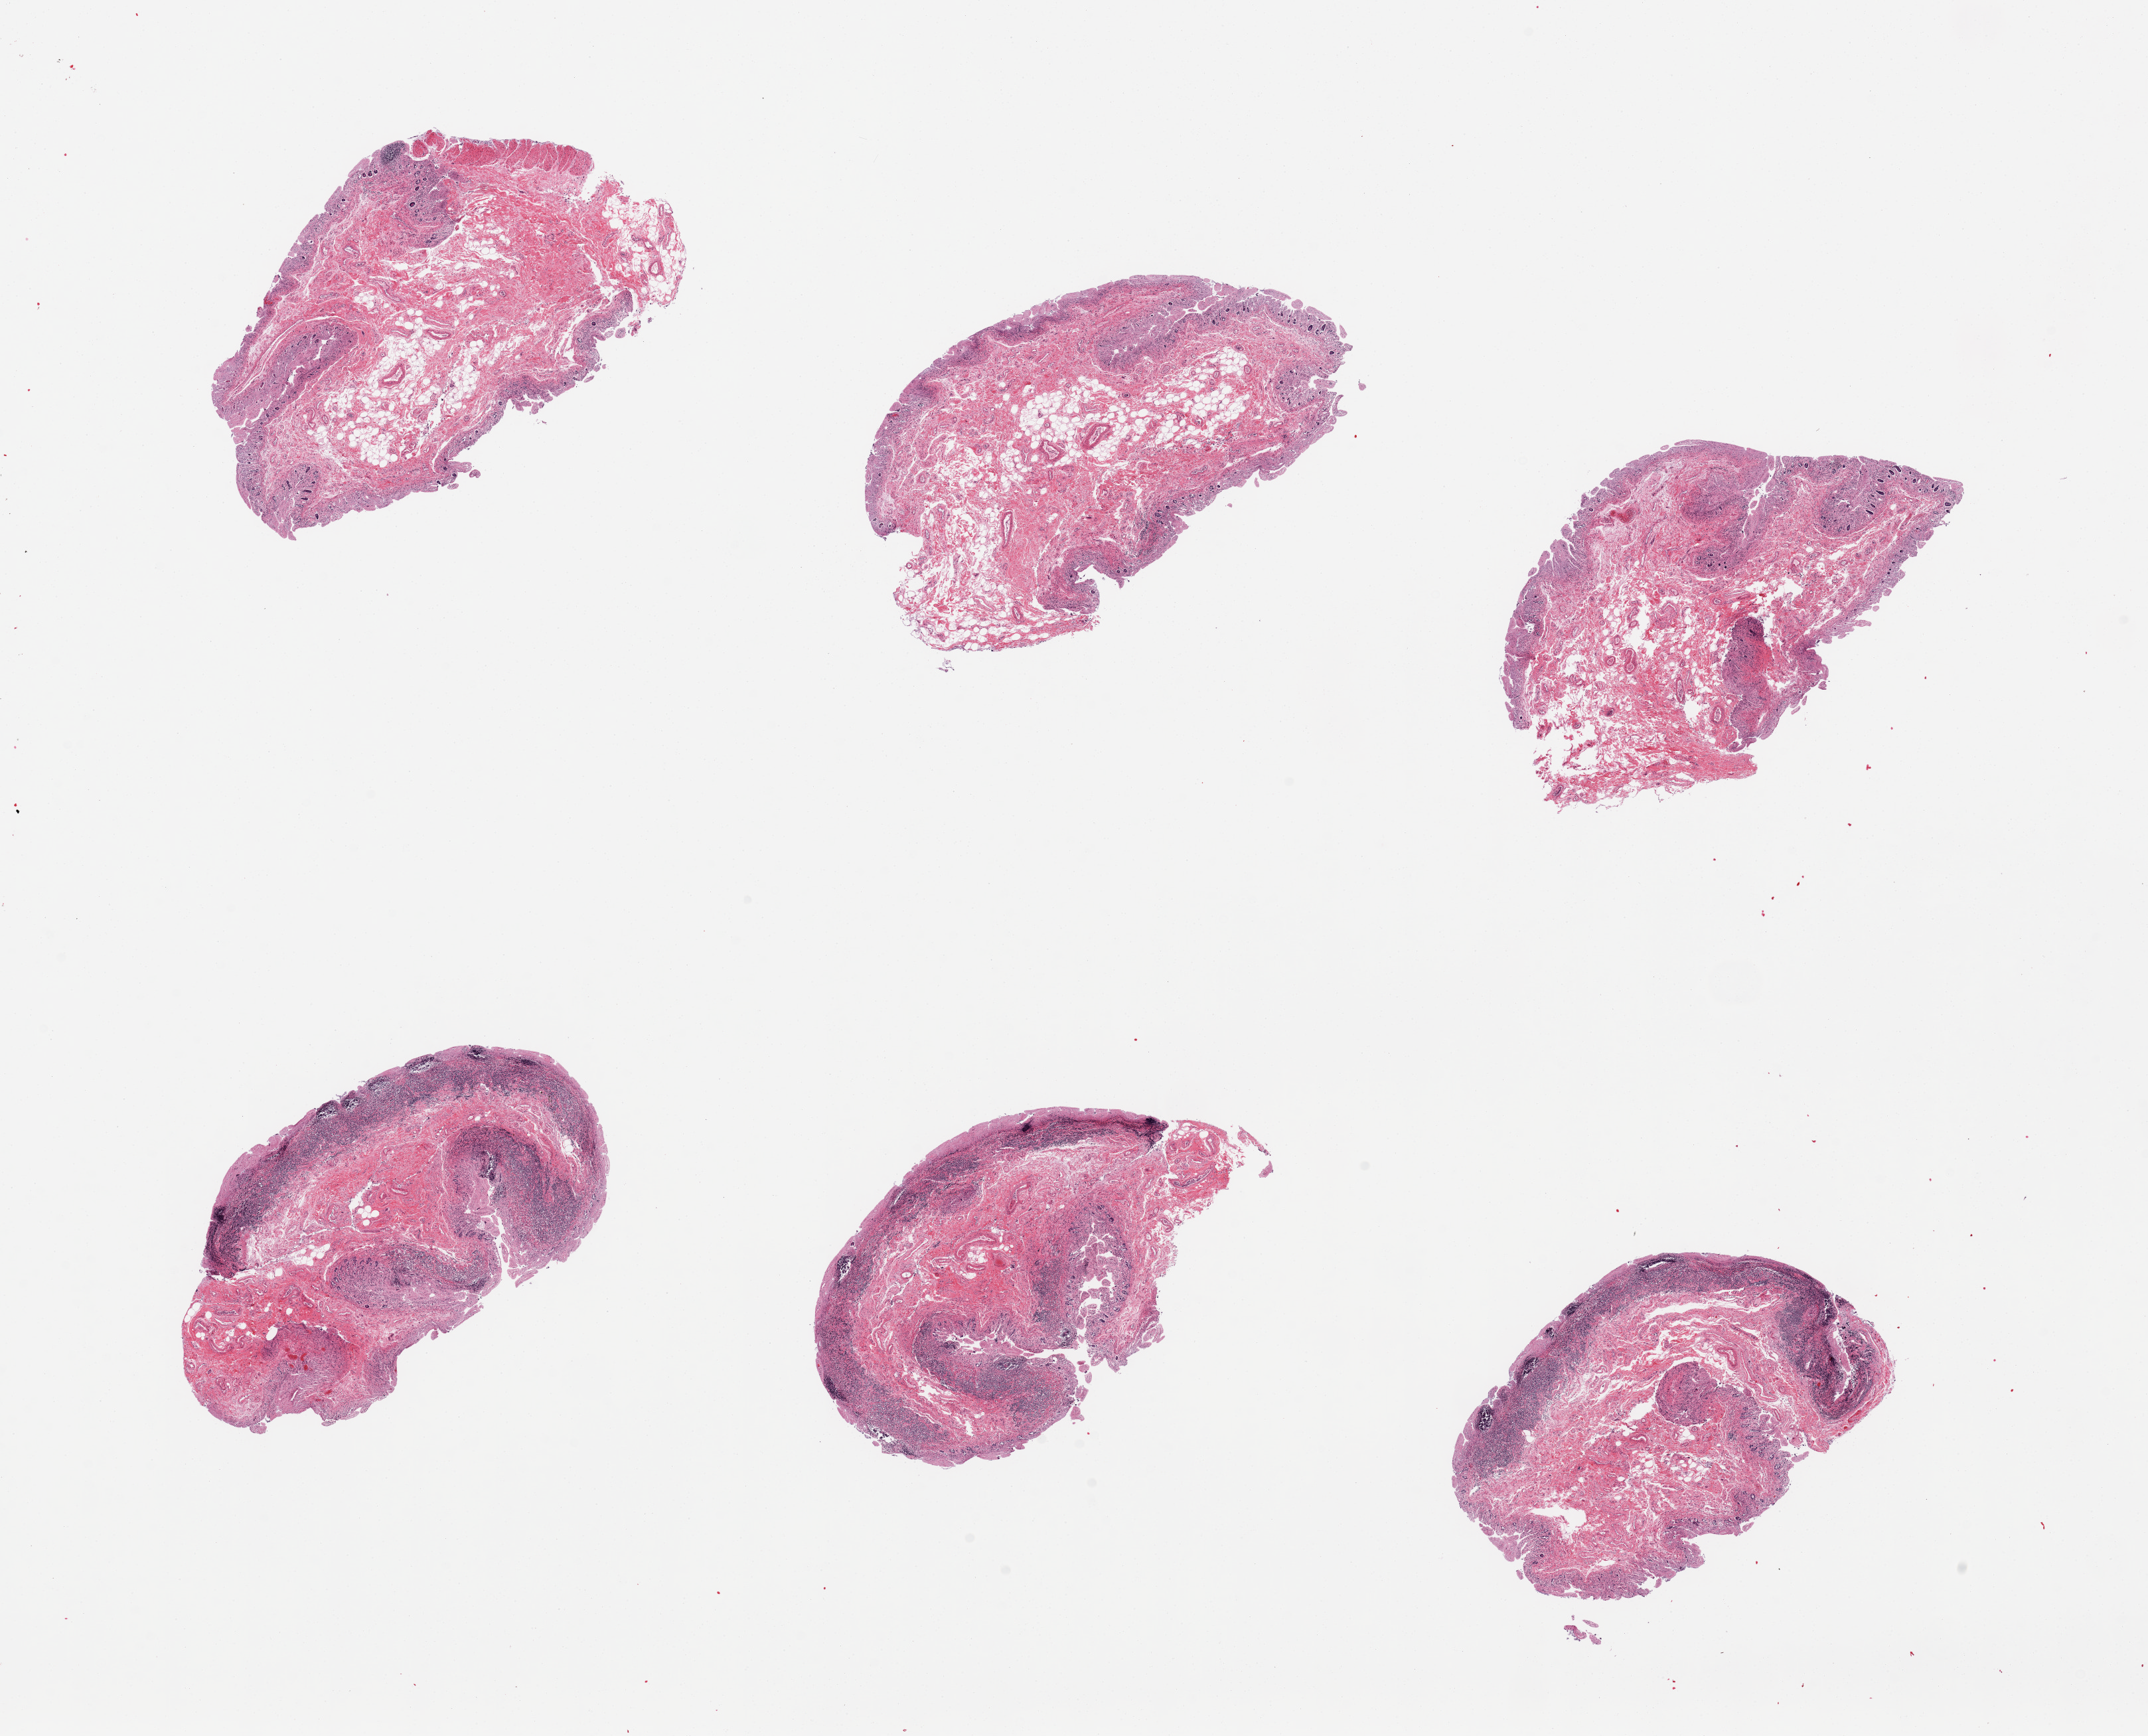
Hematoxylin and eosin (H&E) whole-slide image, low-resolution overview of the scanned area, about 25.6 x 20.7 mm, PAXgene-fixed, paraffin-embedded tissue, section of ileum (target tissue), donor tissue sample. Donor sex: male.
* reviewer comment on this tissue sample: 6 pieces, mucosa epithelium totally autolyzed; ~ abundant residual lympohid aggregates, ~30% total